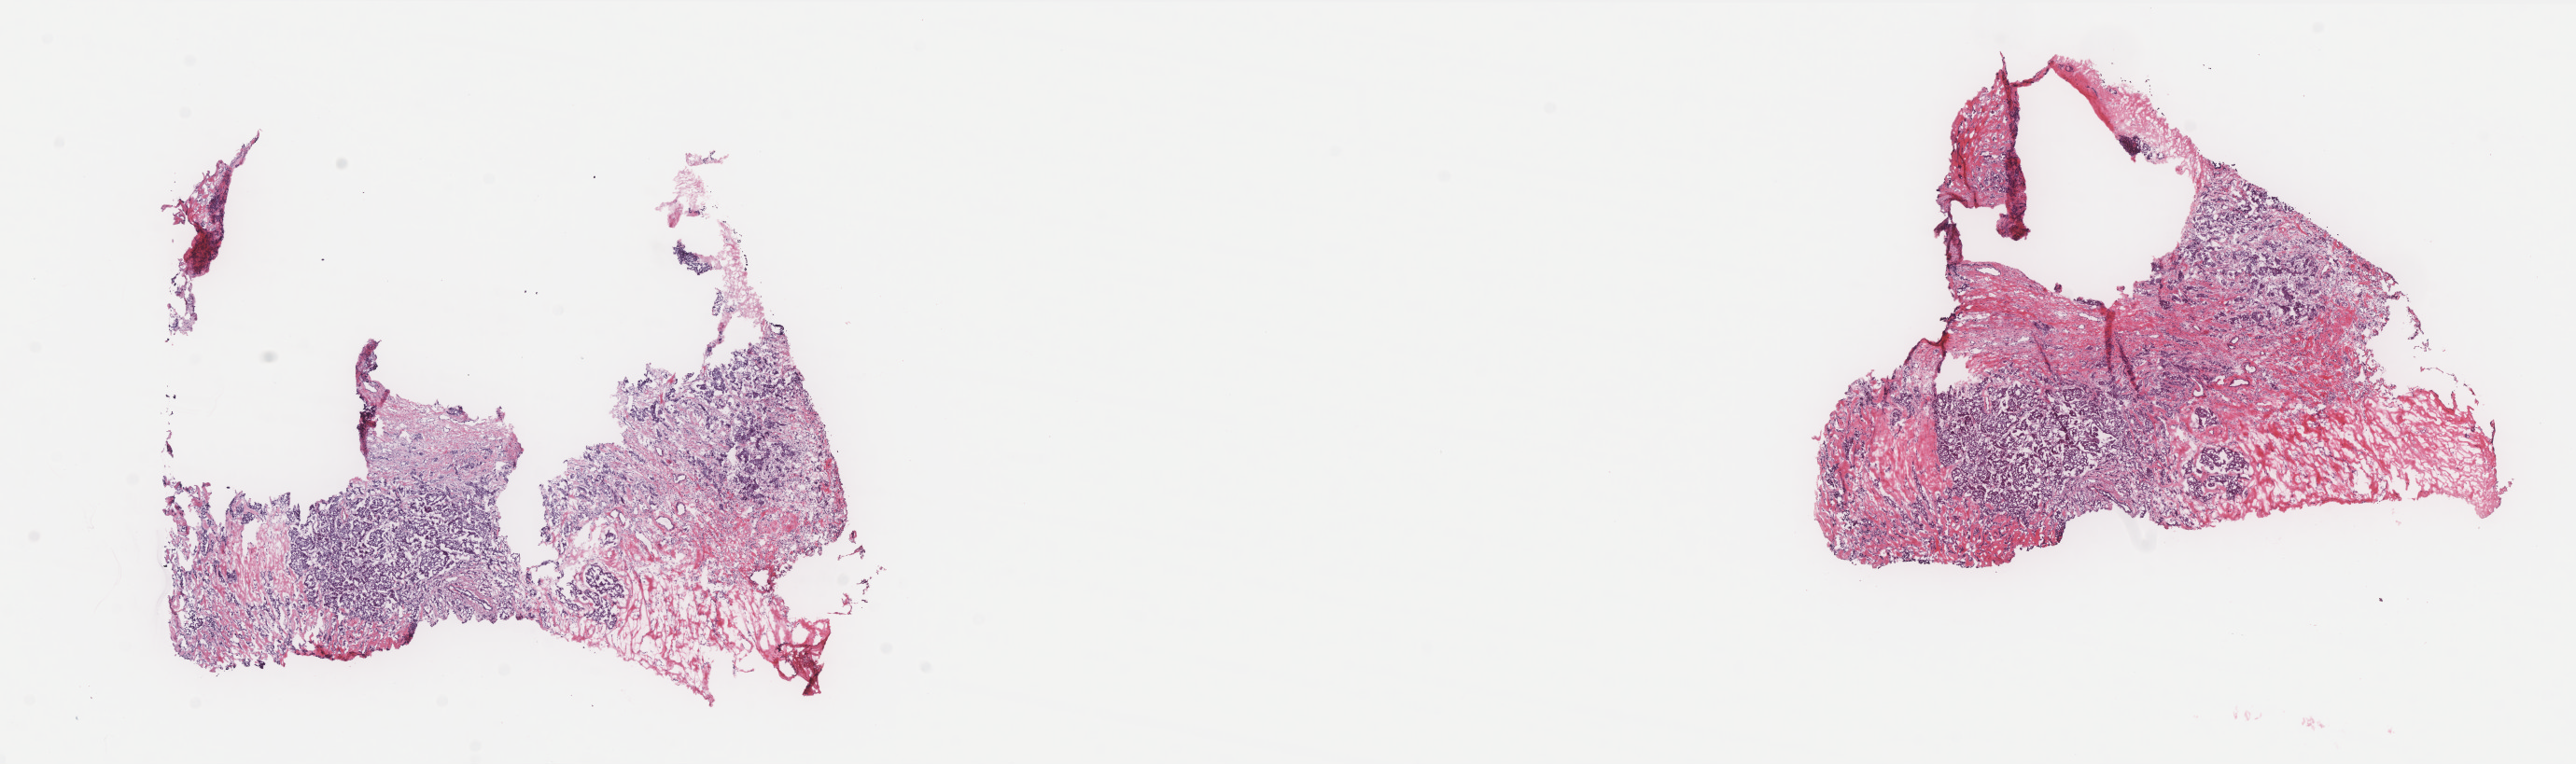
Whole-slide histology image, H&E-stained, a low-resolution overview of the entire scanned area, about 22.1 x 6.6 mm (slide scanned at 40x); frozen section from the bottom of the tissue portion; primary tumour sample from the breast. Patient: female, age at initial diagnosis 58 years. Pathologist review of this section (percent, as recorded): tumour cells 80%, tumour nuclei 80%, normal cells 2%, stromal cells 18%, necrosis 0%. Infiltration values recorded for this section: lymphocyte infiltration 3%, monocyte infiltration 1%, neutrophil infiltration 2%.
• lymph nodes positive (case pathology): 5 of 18 examined
• diagnosis: Infiltrating duct carcinoma, NOS
• laterality: right